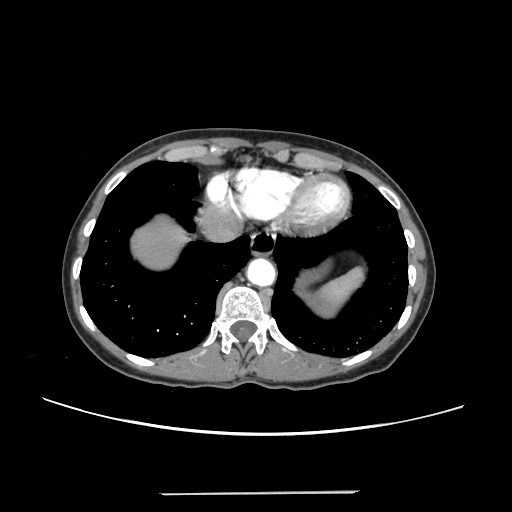
Contrast-enhanced abdominal CT, one axial slice; position 223 of 240 along the scan axis; 120 kVp; intravenous contrast given; soft-tissue window (W 400 / L 40 HU); 1.25 mm slice thickness; 512 × 512 image matrix, field of view 371 × 371 mm. Female patient, age 60 years. From the clinical record (not read from this slice): diagnosis: colorectal cancer liver metastases, imaged before liver resection; multiple liver metastases: no; largest metastasis: 1.5 cm; chemotherapy before resection: yes.
Structures marked on this image (manually delineated by an expert):
- liver: bounding box <134,224,182,267> (left, top, right, bottom; pixels)
- planned liver remnant (the part of the liver to remain after resection): <134,224,182,267>